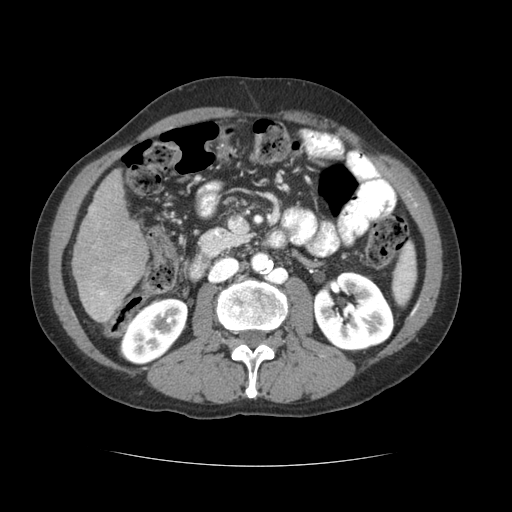
Contrast-enhanced abdominal CT (liver protocol), one axial slice; position 19 of 69 along the scan axis; soft-tissue window (W 400 / L 40 HU); 2.5 mm slice thickness; 512 × 512 image matrix. From the clinical record (not read from this slice): diagnosis: hepatocellular carcinoma (patient treated with transarterial chemoembolisation; whether this scan precedes or follows treatment is not stated here); TNM stage (as recorded): Stage-II; Child-Pugh class: B; tumour differentiation: poorly differentiated; tumour nodularity: multinodular.
Annotated regions visible in this slice (semi-automatic segmentation, software-assisted and operator-edited):
- liver parenchyma outside the tumour (the mass and vessels are separate outlines, so this box may not span the whole liver): box from (x=72, y=170) to (x=148, y=322) px
- liver vessels: (x=91, y=208)–(x=129, y=319)